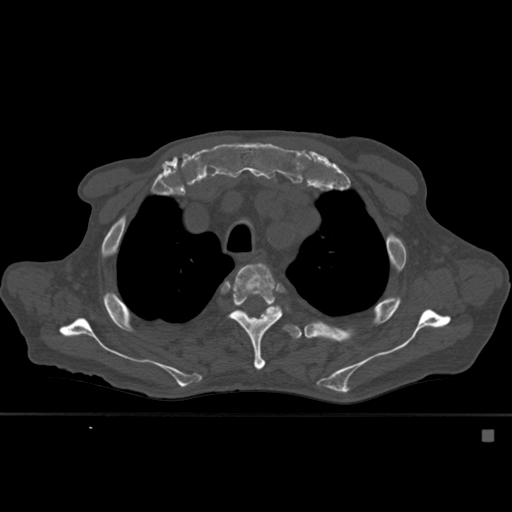
CT including the spine, one axial slice. Position 416 of 527 along the scan axis. Bone window (W 1800 / L 400 HU). 1.5 mm slice thickness. 512 × 512 image matrix. Patient: male, 78 years. Case-level facts recorded for this patient, not image findings: primary cancer: prostate.
Annotated regions visible in this slice (semi-automatically segmented with operator editing):
- T3 vertebra: box from (x=237, y=268) to (x=242, y=275) px
- T4 vertebra: (x=229, y=263)–(x=283, y=370)
- T5 vertebra: (x=237, y=306)–(x=305, y=340)